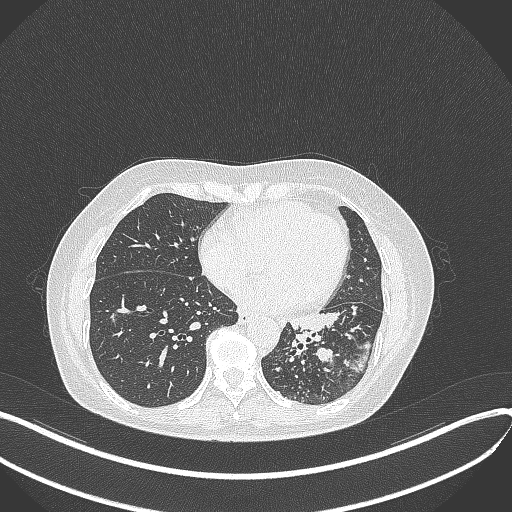
Chest CT, one axial slice; slice 153 of 429 in the series (ordered by position); reconstruction kernel B70f; 100 kVp; lung window (W 1500 / L -600 HU); 512 × 512 image matrix. Female patient, age 63 years. From the clinical record (not read from this slice): clinical TNM (as recorded): T1b N0 M0; histopathological grade: G2-3.
Outlined on this slice (bounding box drawn by a radiologist):
- lung tumour (recorded histology: adenocarcinoma): bounding box (x1, y1, x2, y2) in pixels: (281, 302, 356, 351)